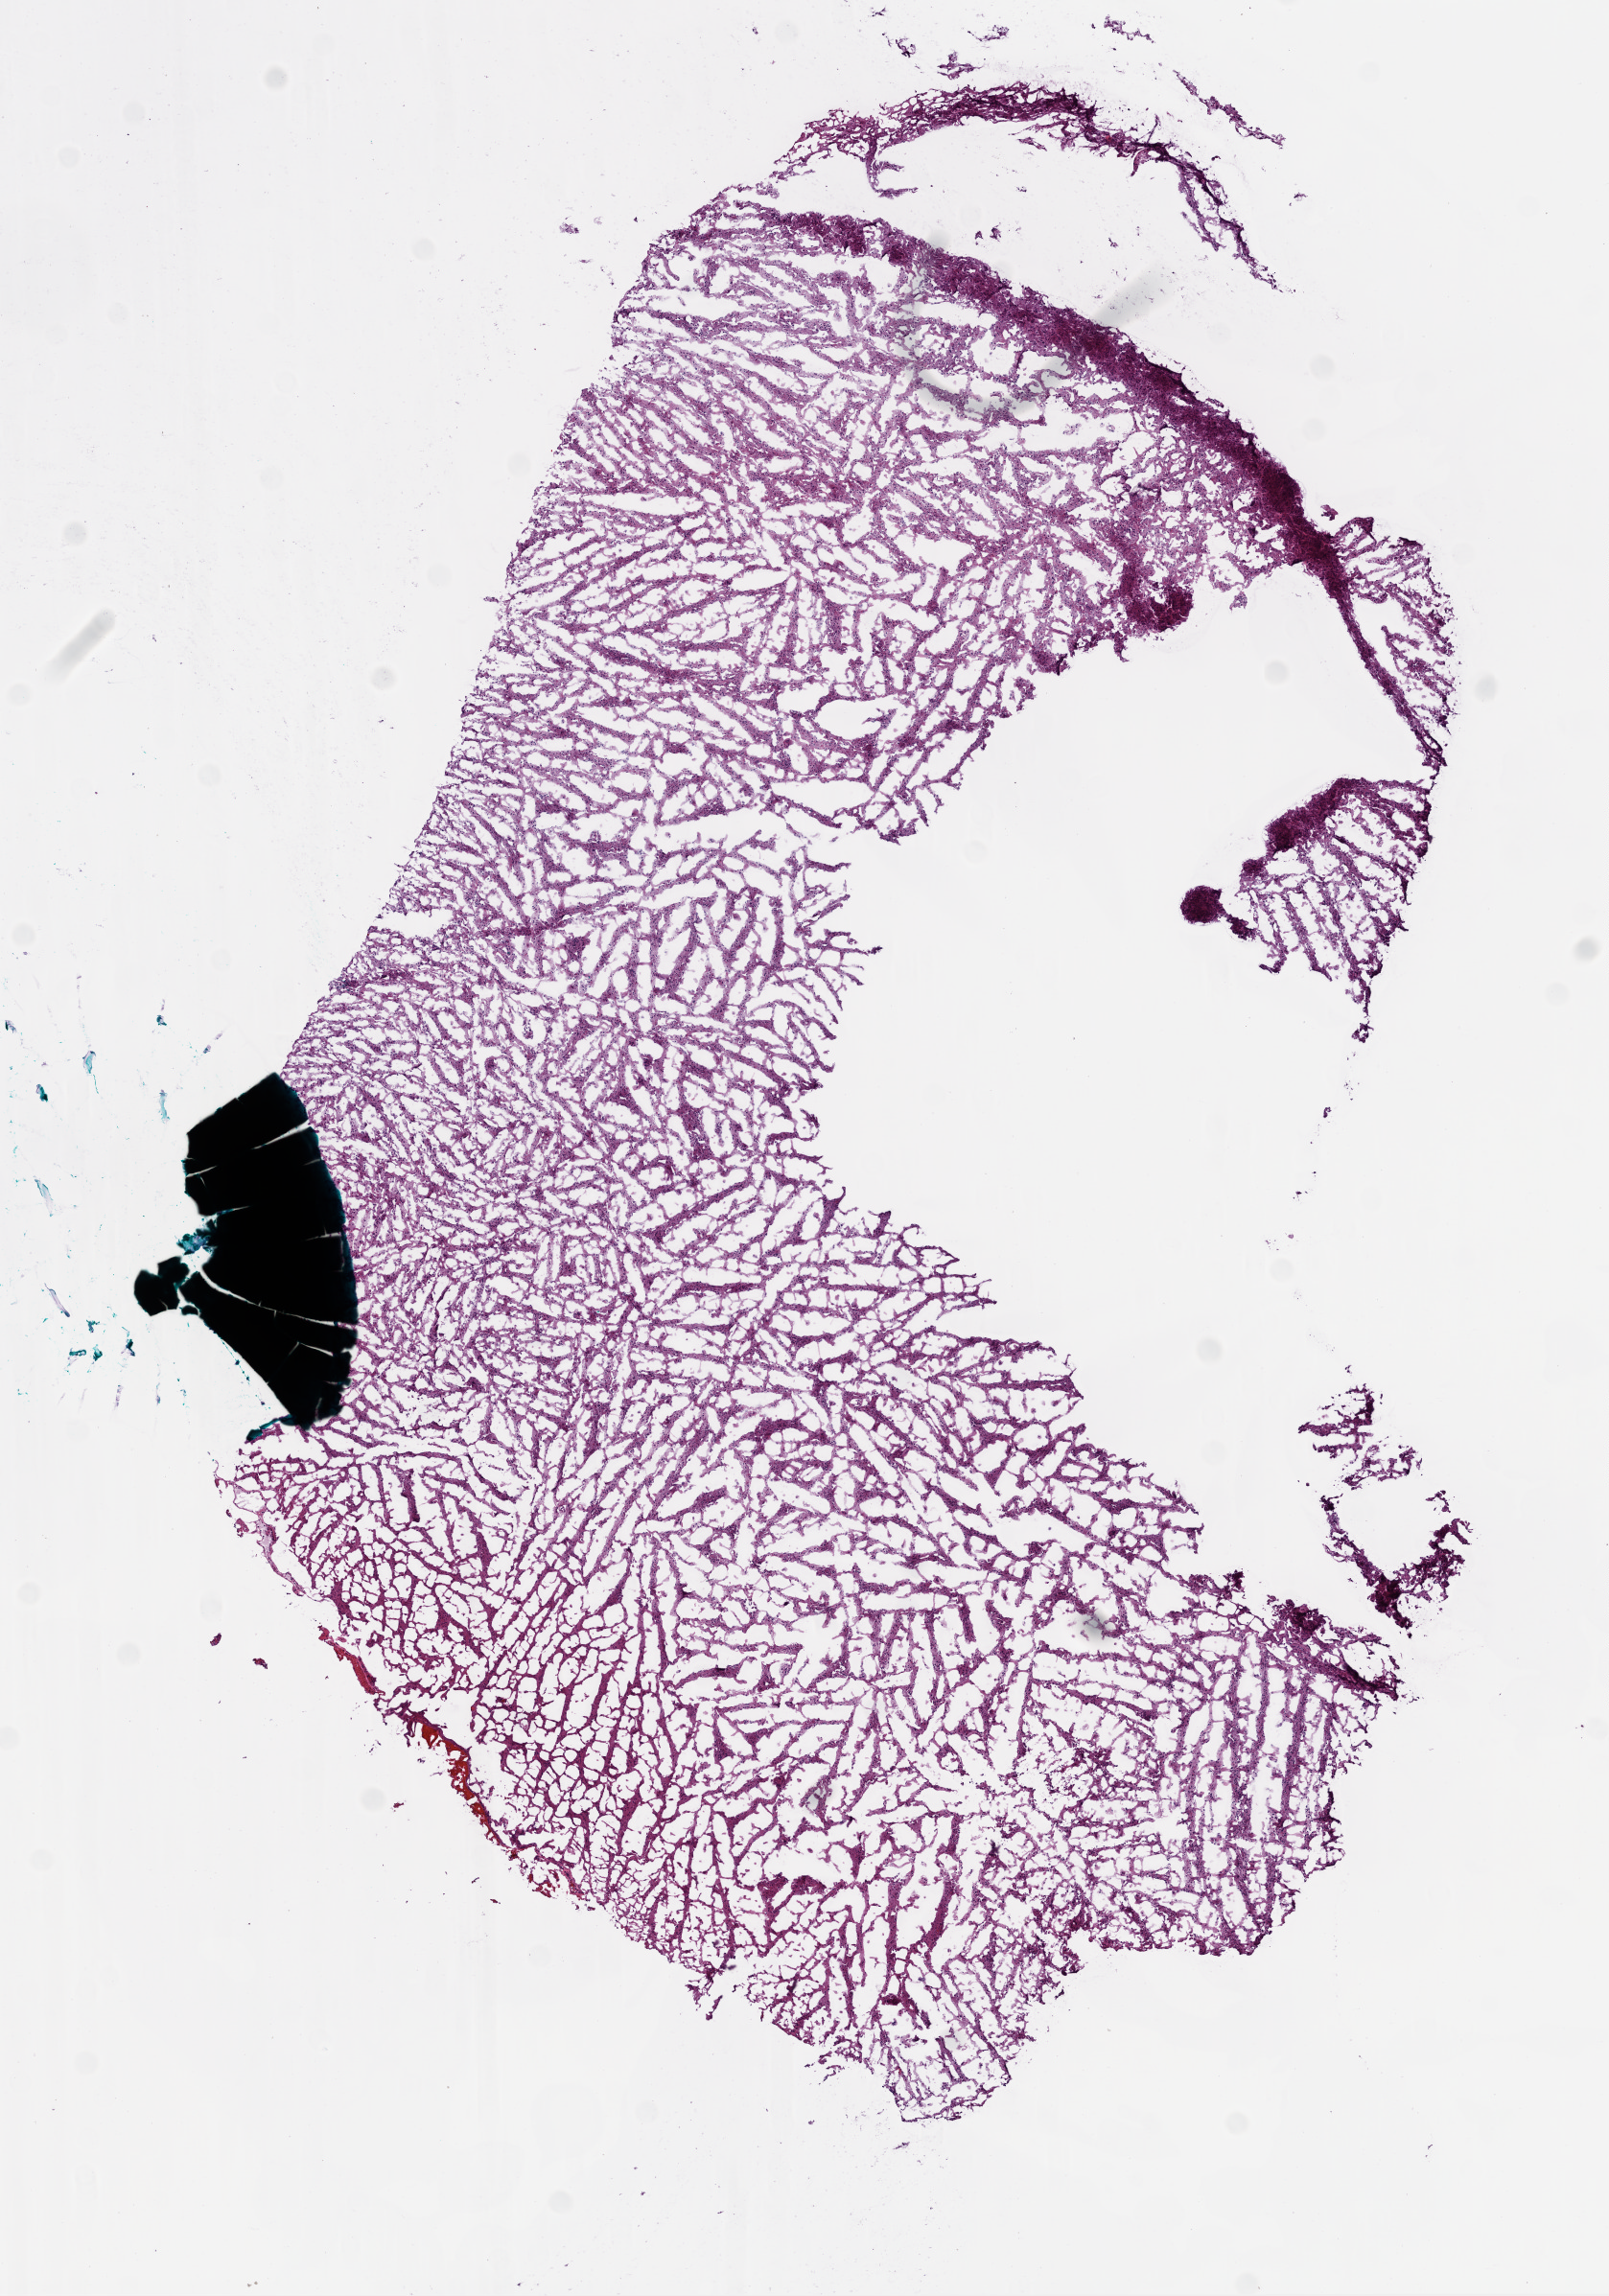
H&E-stained whole-slide image, a low-resolution overview of the entire scanned area, about 6.8 x 9.7 mm, frozen section, brain, primary tumour sample. Male patient; age at initial diagnosis 64 years. Pathologist review of this section (percent, as recorded): tumour cells 75%, tumour nuclei 80%, normal cells 15%, stromal cells 10%, necrosis 0%.
• diagnosis: Glioblastoma